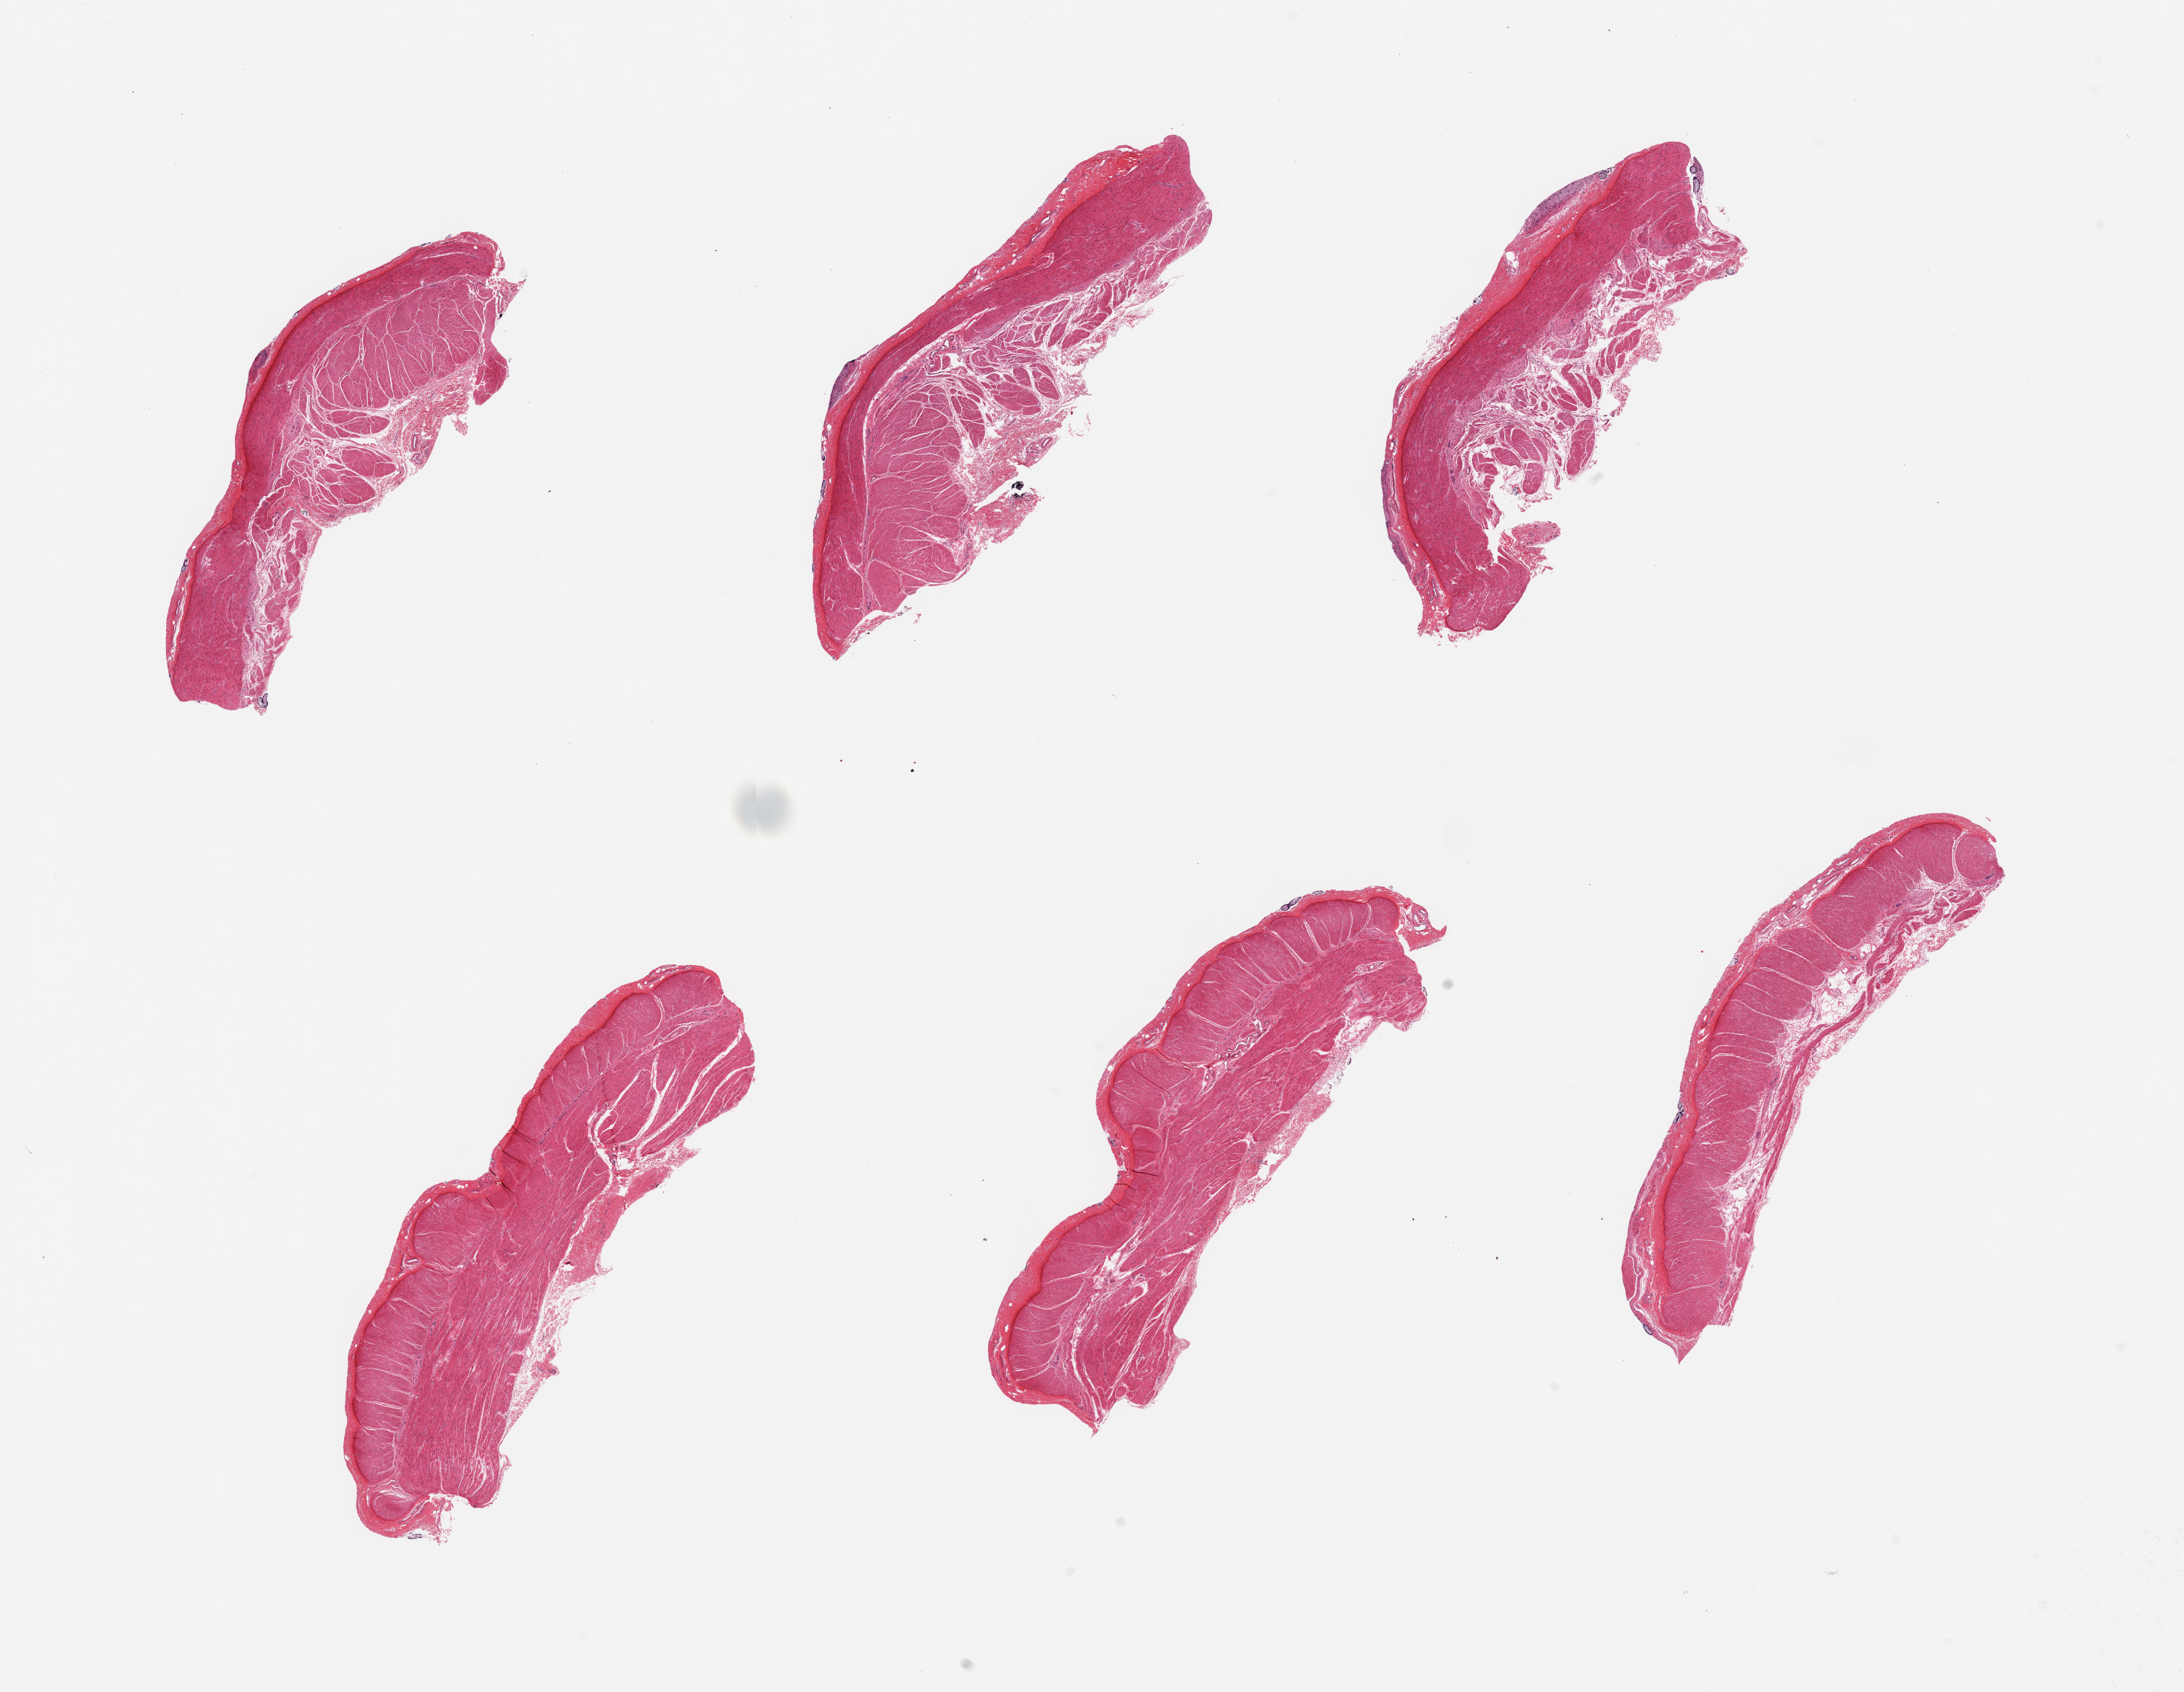
Whole-slide image, haematoxylin and eosin stain, brightfield — low-resolution overview of the scanned area, about 25.6 x 19.8 mm; PAXgene-fixed, paraffin-embedded tissue; section of sigmoid colon (target tissue); tissue donor sample. Donor sex: female.
* review note (as recorded): 6 pieces; <1% glands on surface